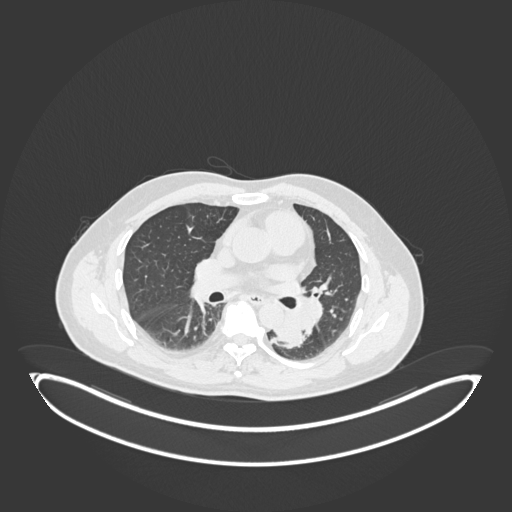
Chest CT, one axial slice. Slice 109 of 258 in the series (ordered by position). Reconstruction kernel B30f. 120 kVp. Lung window (W 1500 / L -600 HU). 1 mm slice thickness. 512 × 512 image matrix, field of view 500 × 500 mm. Patient: male, 54 years. From the clinical record (not read from this slice): clinical TNM (as recorded): T3 N0 M0.
Structures marked on this image (bounding box drawn by a radiologist):
- lung tumour (recorded histology: squamous cell carcinoma): bounding box (x1, y1, x2, y2) in pixels: (273, 308, 307, 351)